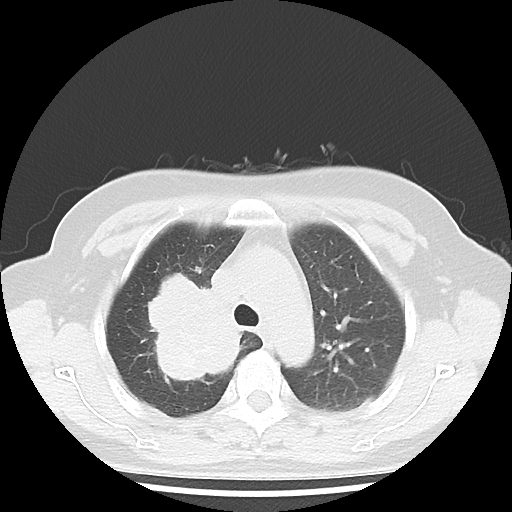
Chest CT, one axial slice; slice 31 of 43 in the series (ordered by position); reconstruction kernel LUNG; lung window (W 1500 / L -600 HU); 5 mm slice thickness; 512 × 512 image matrix, field of view 316 × 316 mm. Female patient, age 62 years. From the clinical record (not read from this slice): clinical TNM (as recorded): T3 N0 M0.
Structures marked on this image (bounding box drawn by a radiologist):
- lung tumour (recorded histology: small cell carcinoma): bounding box [x1, y1, x2, y2] px = [131, 263, 250, 392]